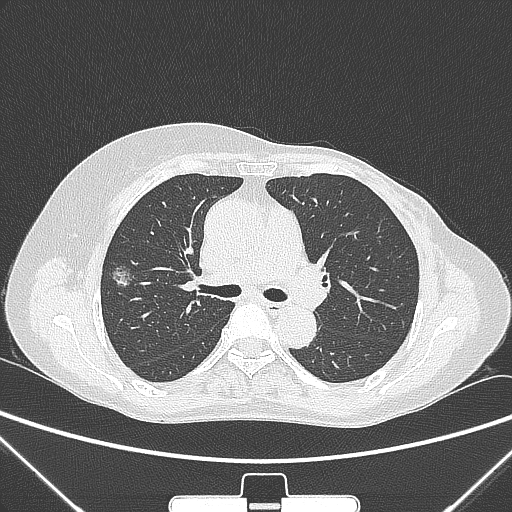
Chest CT, one axial slice; position 158 of 265 along the scan axis; lung window (W 1500 / L -600 HU); 1 mm slice thickness; 512 × 512 image matrix. Patient: female, 64 years. From the clinical record (not read from this slice): clinical TNM (as recorded): T1c N0 M0.
Annotated regions visible in this slice (rectangle marked by the reading radiologist):
- lung tumour (recorded histology: adenocarcinoma): bounding box (x1, y1, x2, y2) in pixels: (107, 260, 134, 289)